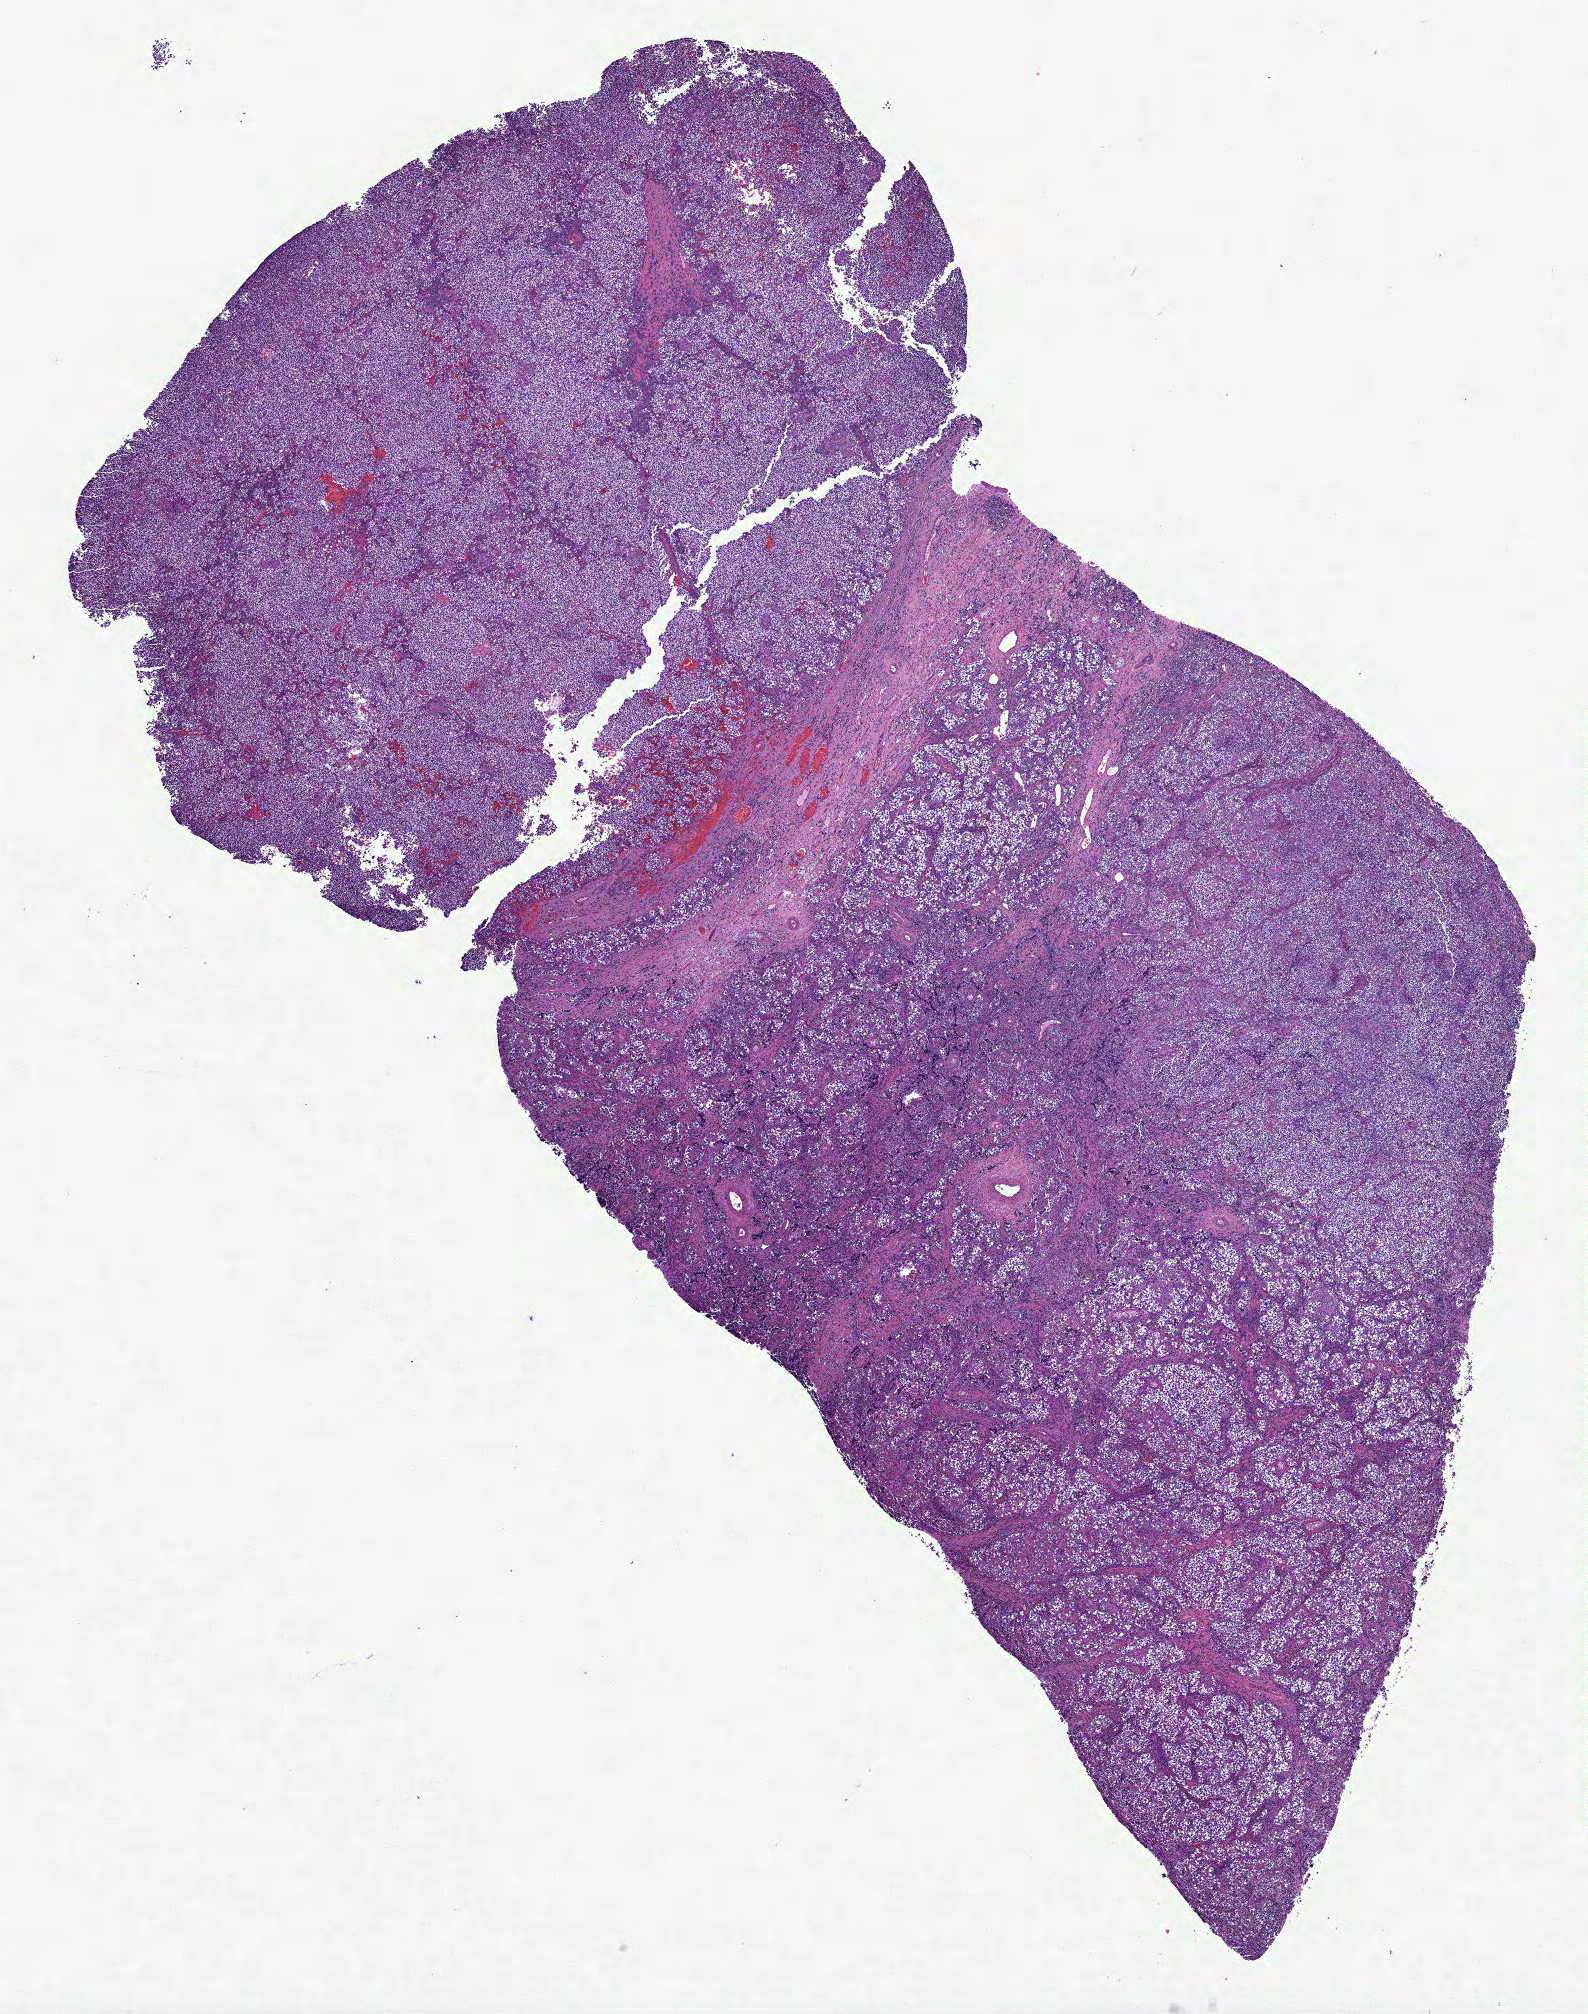
Digitized Hematoxylin and eosin (H&E) stained tissue section (whole slide) — low-resolution overview of the scanned area, about 12.8 x 16.2 mm; FFPE section; testis, primary tumour sample. Male, age 20 years at initial diagnosis.
- laterality: right
- histologic diagnosis: Seminoma, NOS
- AJCC pathologic stage: I (7th edition)